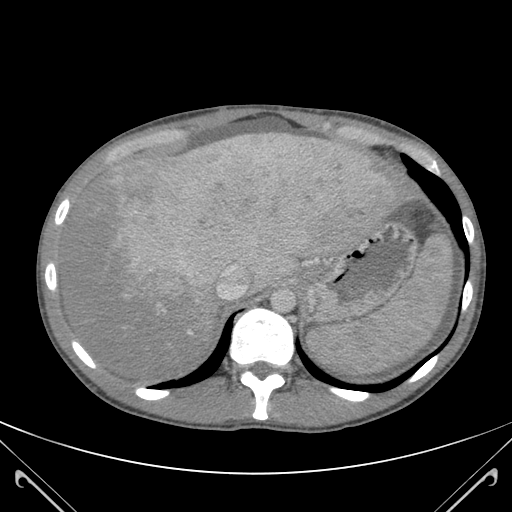
Contrast-enhanced abdominal CT (liver protocol), one axial slice; position 93 of 118 along the scan axis; 120 kVp; soft-tissue window (W 400 / L 40 HU); 3 mm slice thickness; 512 × 512 image matrix, field of view 380 × 380 mm. From the clinical record (not read from this slice): diagnosis: hepatocellular carcinoma (patient treated with transarterial chemoembolisation; whether this scan precedes or follows treatment is not stated here); TNM stage (as recorded): Stage-IIIB; Child-Pugh class: A.
Annotated regions visible in this slice (semi-automatic segmentation, software-assisted and operator-edited):
- abdominal aorta: box from (x=273, y=289) to (x=295, y=312) px
- liver parenchyma outside the tumour (the mass and vessels are separate outlines, so this box may not span the whole liver): (x=62, y=132)–(x=422, y=378)
- mass: (x=99, y=133)–(x=387, y=305)
- liver vessels: (x=163, y=143)–(x=385, y=334)